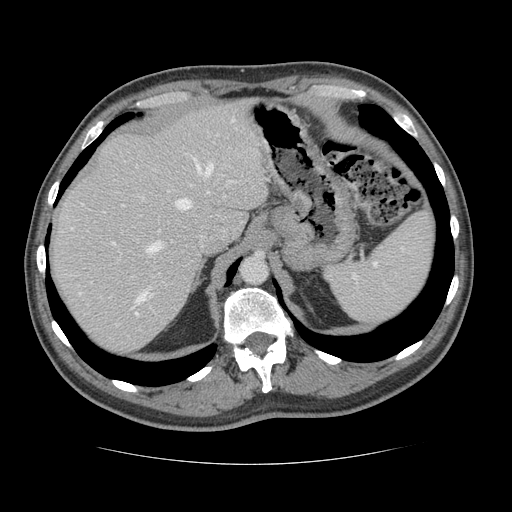
Contrast-enhanced abdominal CT, one axial slice; slice 98 of 134 in the series (ordered by position); reconstruction kernel STANDARD; 120 kVp; intravenous contrast given; soft-tissue window (W 400 / L 40 HU); 2.5 mm slice thickness; 512 × 512 image matrix. Male patient, age 68 years. Case-level facts recorded for this patient, not image findings: diagnosis: colorectal cancer liver metastases, imaged before liver resection; multiple liver metastases: yes; largest metastasis: 2.2 cm; disease in both lobes: no.
Annotated regions visible in this slice (outlined manually by an expert reader):
- hepatic veins: bounding box [x1, y1, x2, y2] px = [79, 163, 213, 315]
- liver: [52, 102, 268, 354]
- planned liver remnant (the part of the liver to remain after resection): [51, 102, 268, 327]
- portal vein (with intrahepatic branches): [112, 181, 233, 296]